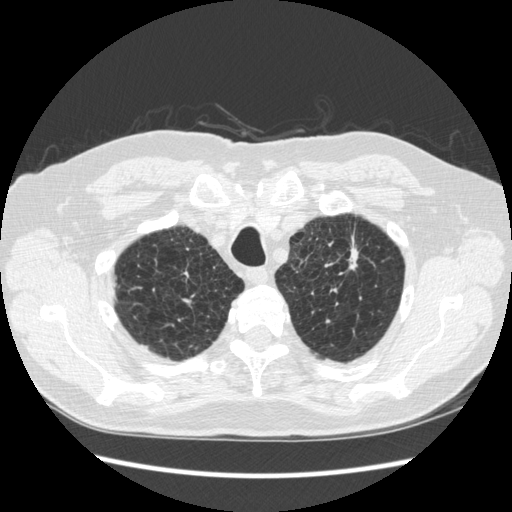
Chest CT (low-dose screening protocol), one axial image; third annual screen; lung window (W 1500 / L -600 HU); standard (soft-tissue) reconstruction kernel (STANDARD); slice 38 of 267 in the series; 512 × 512 image matrix. Male participant, aged 70 years at enrolment.
- Expert reader's lesion annotation, bounding box <324,225,377,290> (left, top, right, bottom; pixels).
- The screening reader recorded 2 non-calcified nodules or masses ≥4 mm on this exam (left upper lobe, right lower lobe); which of them this box marks is not recorded.
- Participant outcome: lung cancer diagnosed 92 days after this screen — squamous cell carcinoma, NOS, left upper lobe, moderately differentiated (G2), stage IA (AJCC 6th edition), 18 mm at pathology.